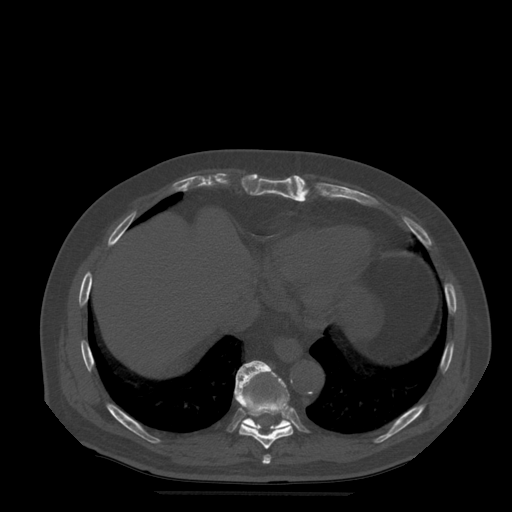
CT including the spine, one axial slice. Position 283 of 522 along the scan axis. Bone window (W 1800 / L 400 HU). 1.25 mm slice thickness. 512 × 512 image matrix. Patient age 72 years. Case-level facts recorded for this patient, not image findings: primary cancer: prostate.
Outlined on this slice (semi-automatic segmentation, software-assisted and operator-edited):
- T10 vertebra: bounding box (x1, y1, x2, y2) in pixels: (236, 361, 290, 431)
- T8 vertebra: (263, 455, 272, 465)
- T9 vertebra: (235, 363, 294, 449)